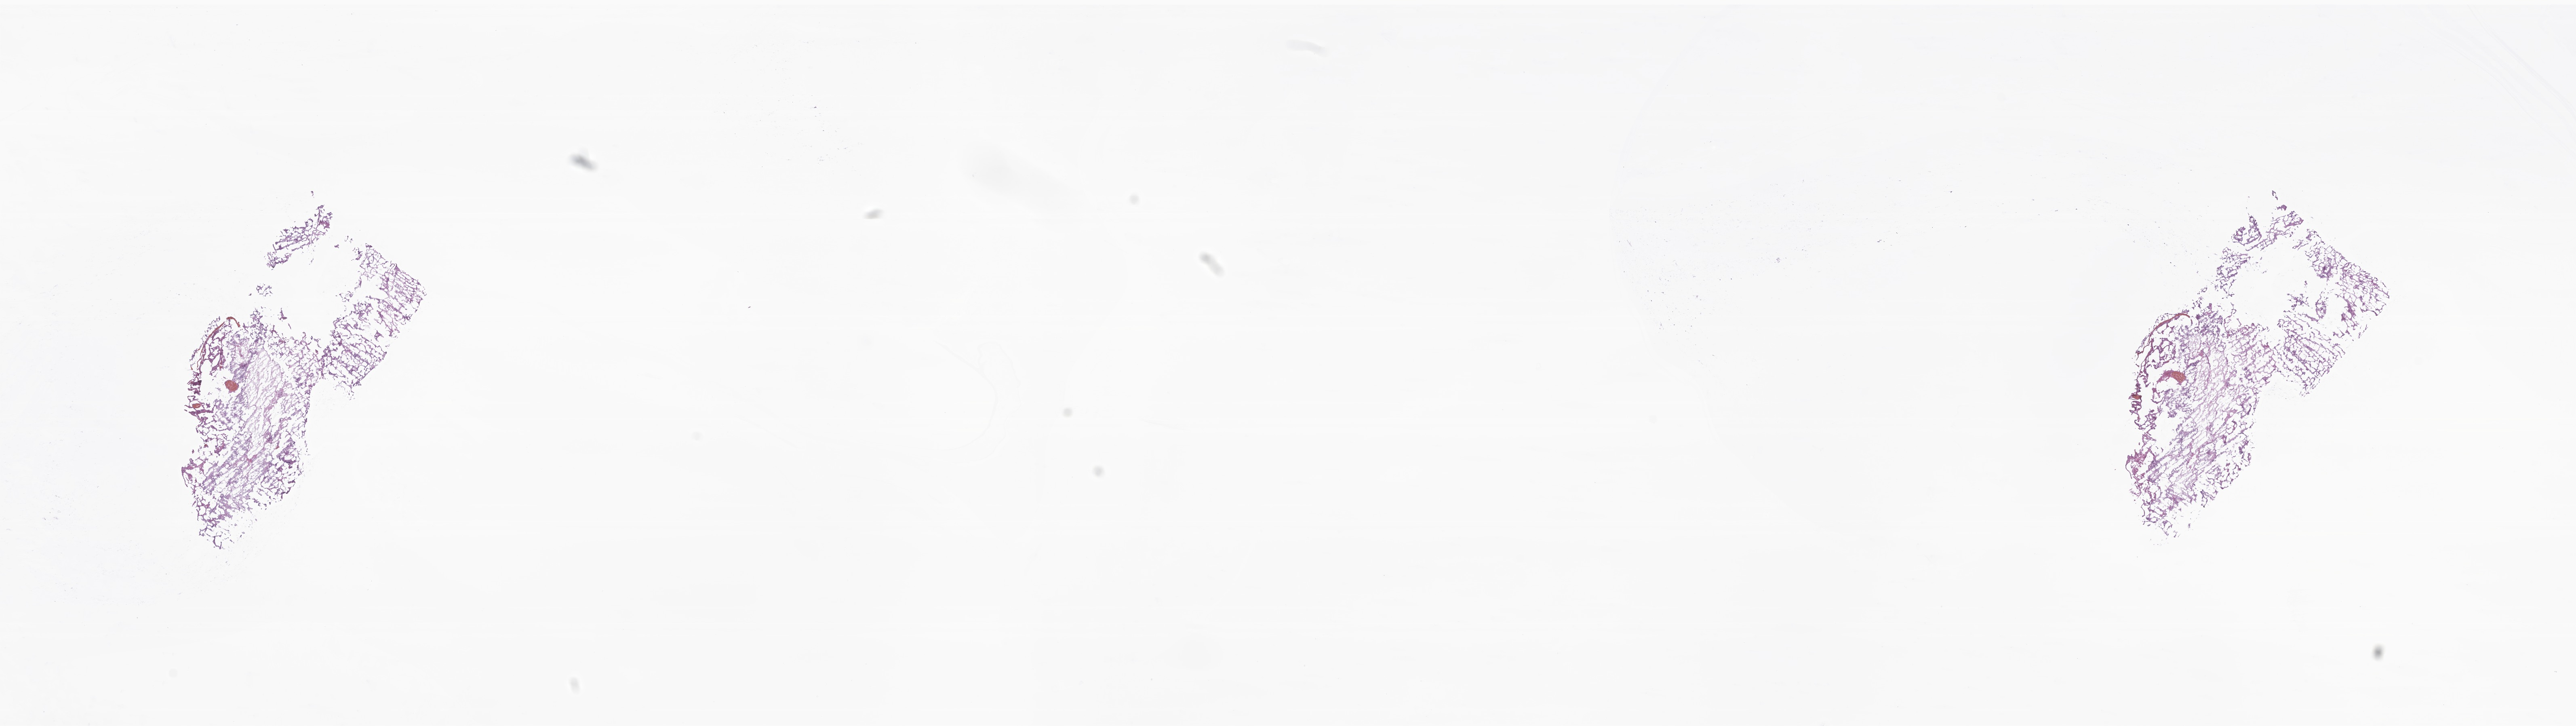
Digitized haematoxylin and eosin-stained section of tumor tissue from the brain — low-resolution overview of the scanned area, about 26.9 x 7.6 mm. Frozen section (OCT-embedded). Patient: male, age 631 days (about 1.7 years).
* diagnosis (ICD-O-3 morphology term): Ependymoma, NOS